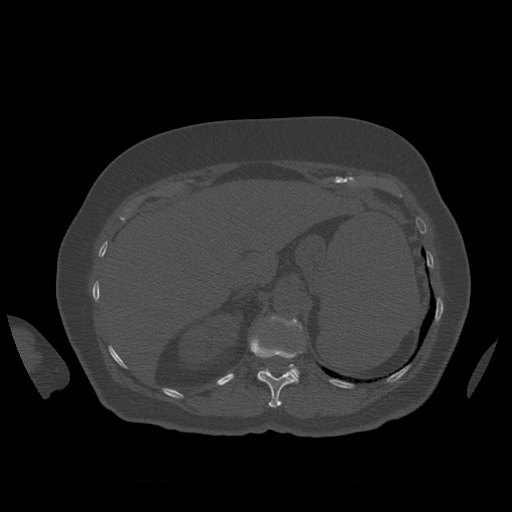
CT including the spine, one axial slice; position 295 of 399 along the scan axis; bone window (W 1800 / L 400 HU); 512 × 512 image matrix. Patient age 81 years. Case-level facts recorded for this patient, not image findings: primary cancer: renal; vertebrae with lytic lesions (as recorded): L1.
Outlined on this slice (semi-automatically segmented with operator editing):
- L1 vertebra: bounding box (x1, y1, x2, y2) in pixels: (269, 317, 303, 378)
- T12 vertebra: (251, 337, 302, 408)